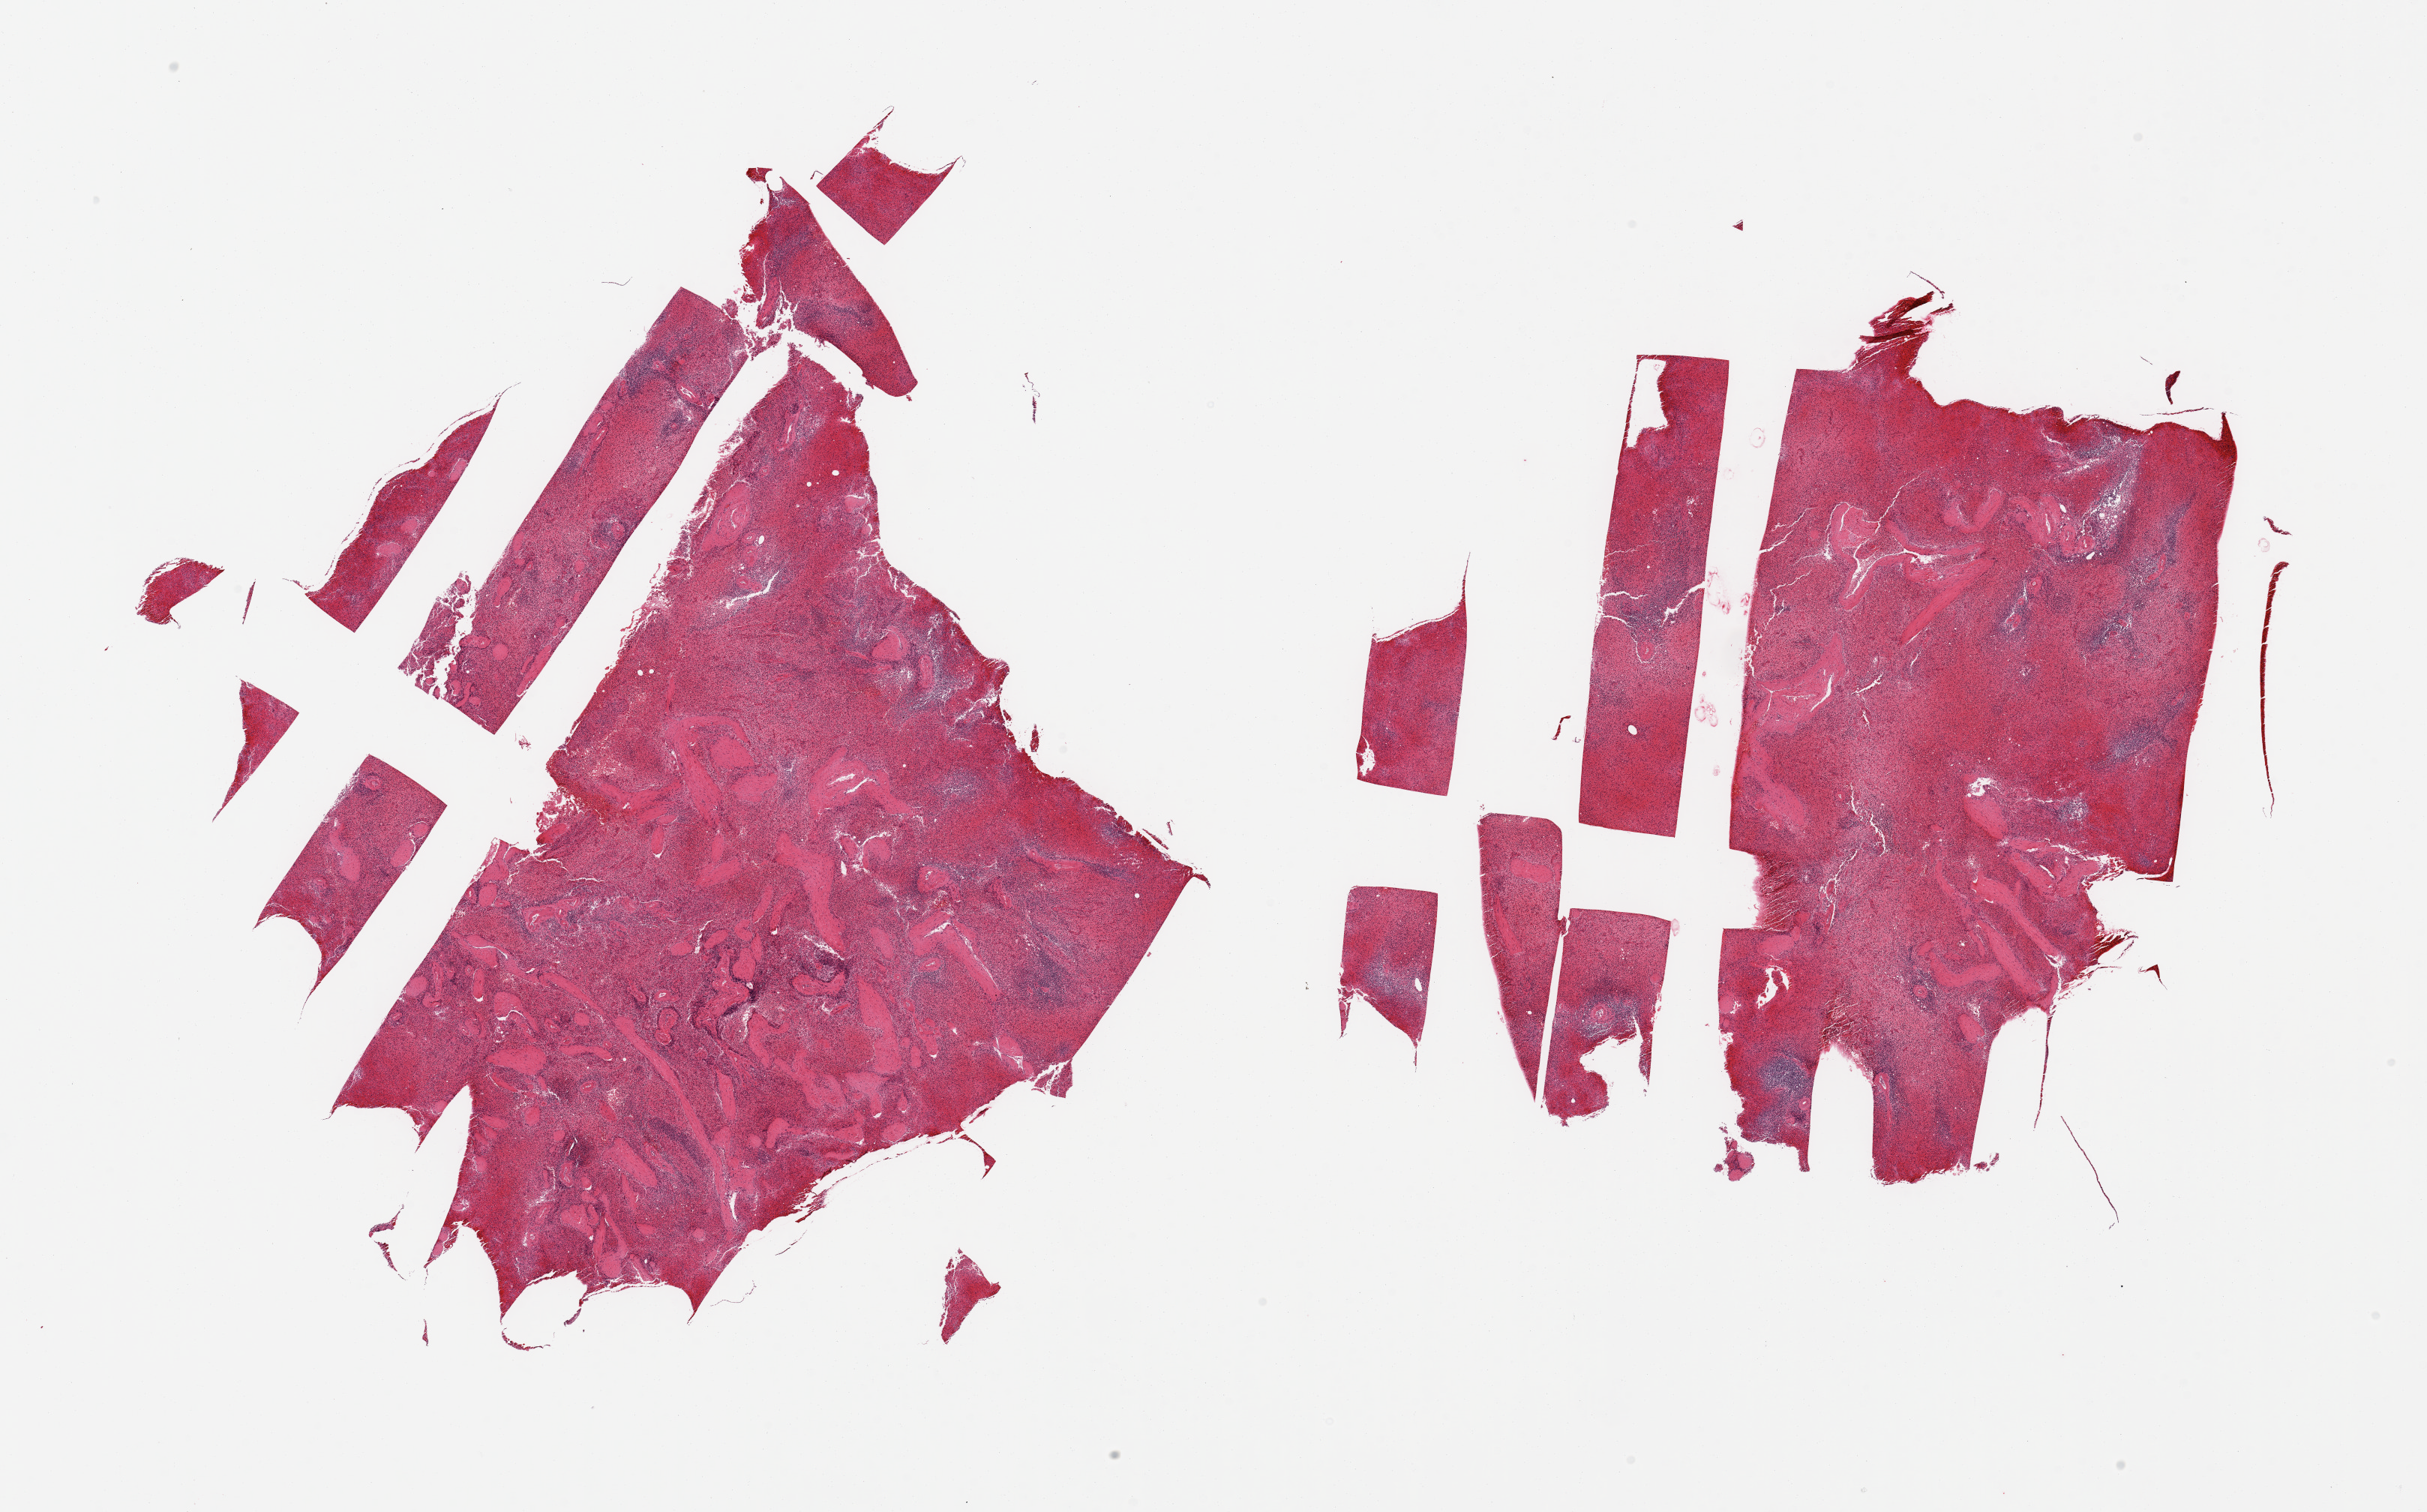
Digitized haematoxylin and eosin-stained section — shown as a low-resolution overview of the whole scanned area (about 25.6 x 15.9 mm, from a 20x scan), PAXgene-fixed, paraffin-embedded tissue, sampled site (target tissue): spleen, tissue donor sample. Donor: male.
Reviewer comment on this tissue sample: 2 fragmented pieces; congestion.